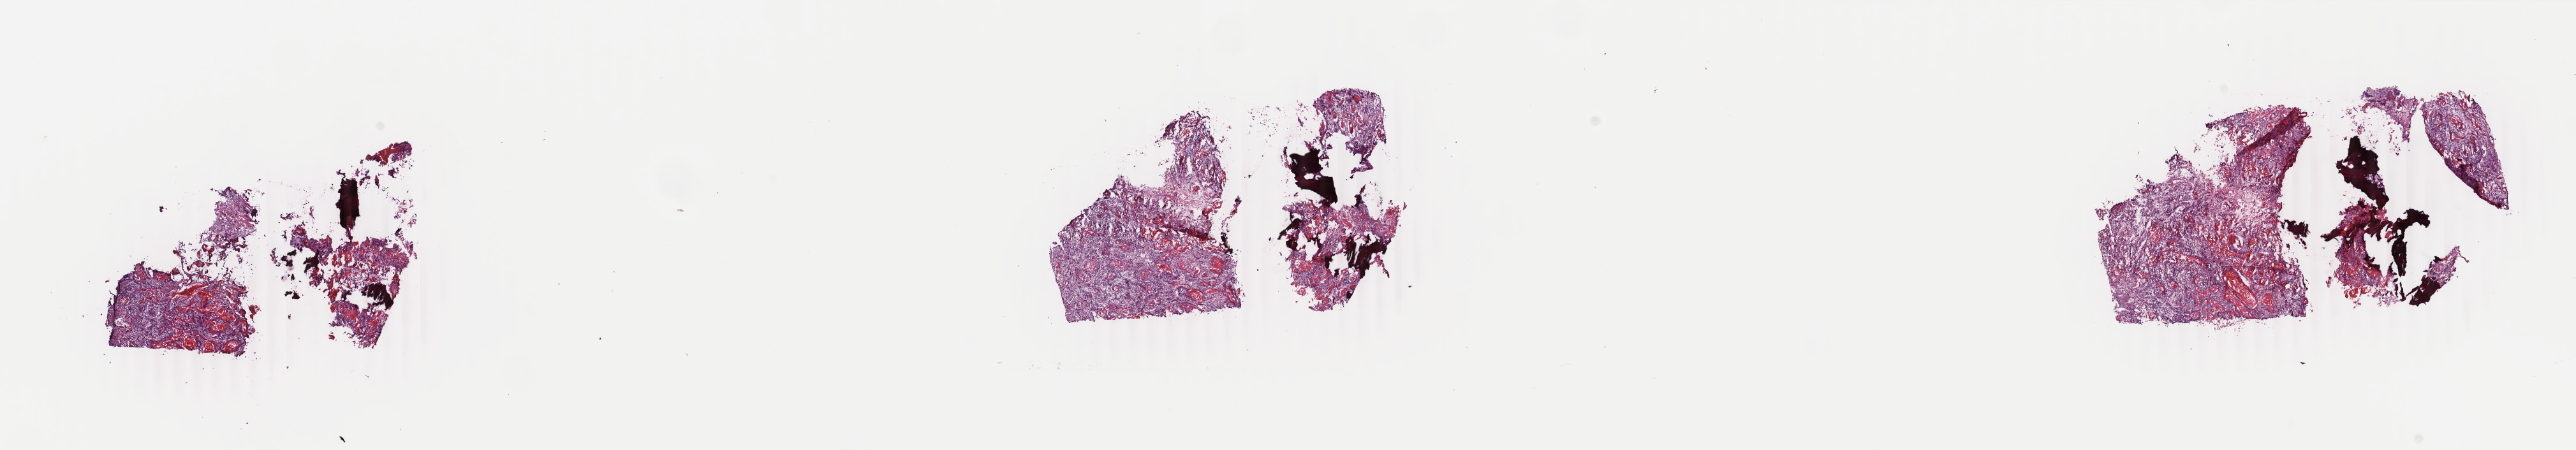
H&E-stained whole-slide image — low-resolution overview of the scanned area, about 32.1 x 5.6 mm (from a 40x scan); frozen section from the top of the tissue portion; sample: primary tumour, head and neck. Female, age 82 years at initial diagnosis. Histologic grade: G2 (moderately differentiated). Composition of this section per pathologist review: tumour cells 70%, tumour nuclei 70%, normal cells 0%, stromal cells 29%, necrosis 1%. Inflammatory infiltration, as recorded: lymphocyte infiltration 4%, monocyte infiltration 2%, neutrophil infiltration 6%.
- diagnosis: Squamous cell carcinoma, keratinizing, NOS
- AJCC pathologic stage: IVA
- lymph nodes positive (case pathology): 4 of 61 examined
- laterality: right